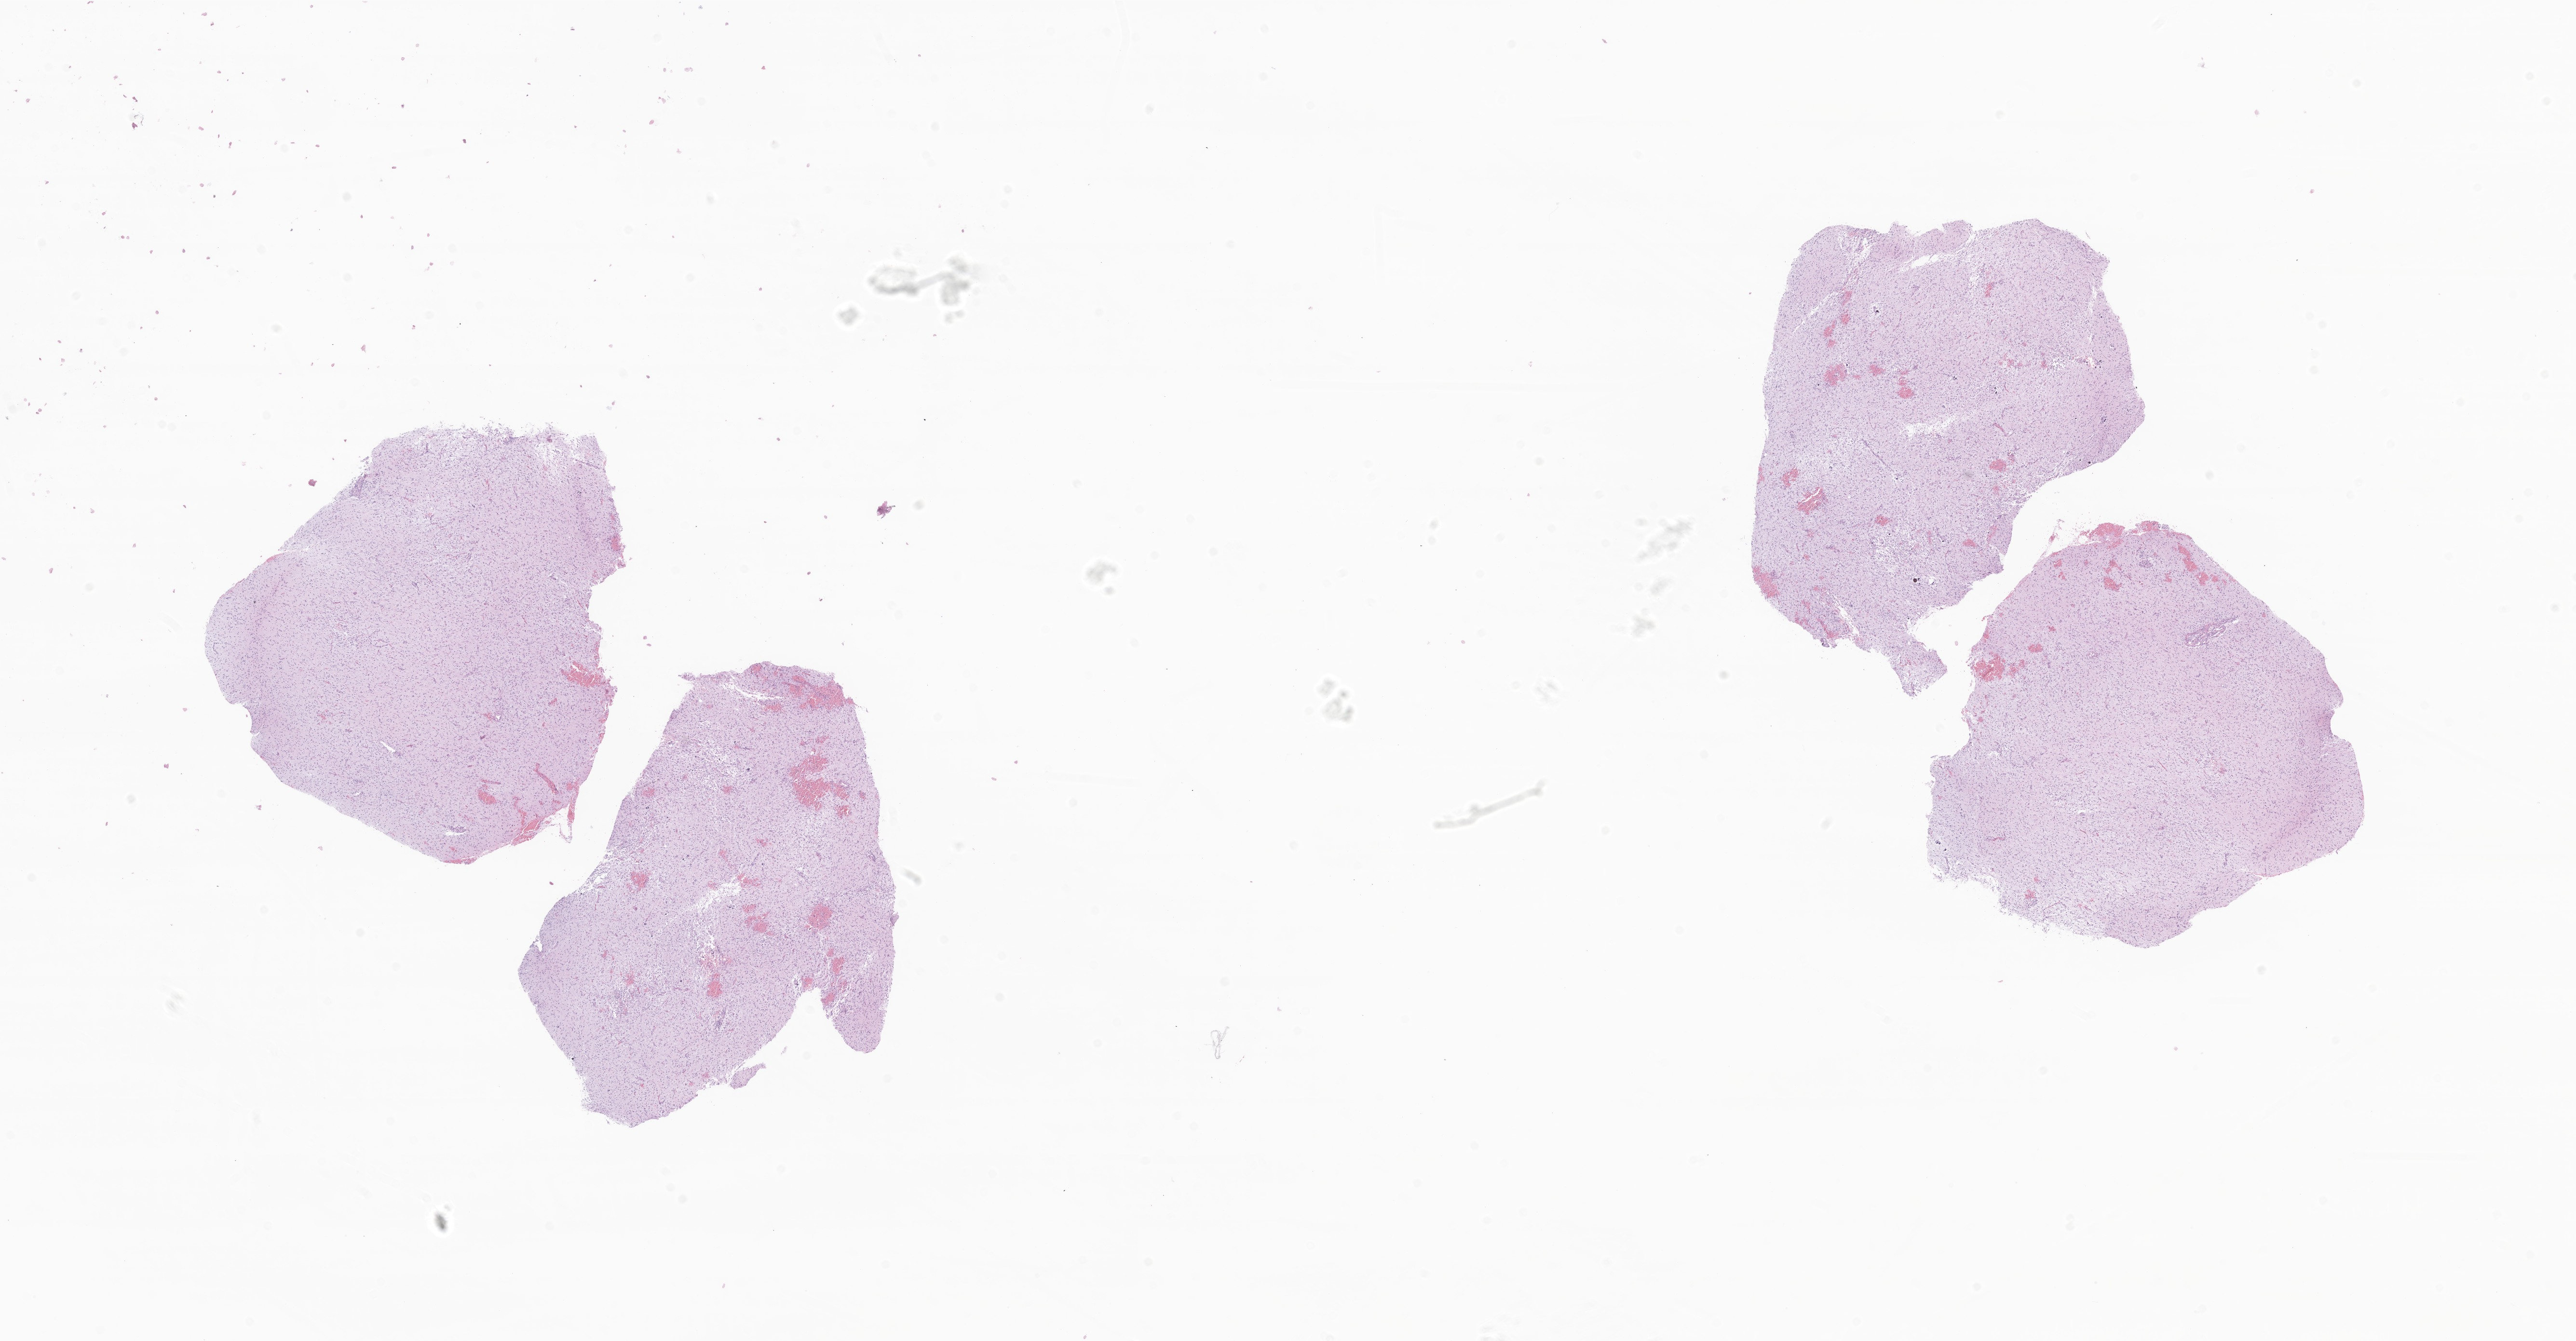
Haematoxylin and eosin whole-slide image of tumor tissue from the temporal lobe, a low-resolution overview of the entire scanned area, about 22.5 x 11.7 mm, formalin-fixed paraffin-embedded section. Patient male; age 732 days (about 2.0 years).
Diagnosis (ICD-O-3 morphology term): Neoplasm, malignant.